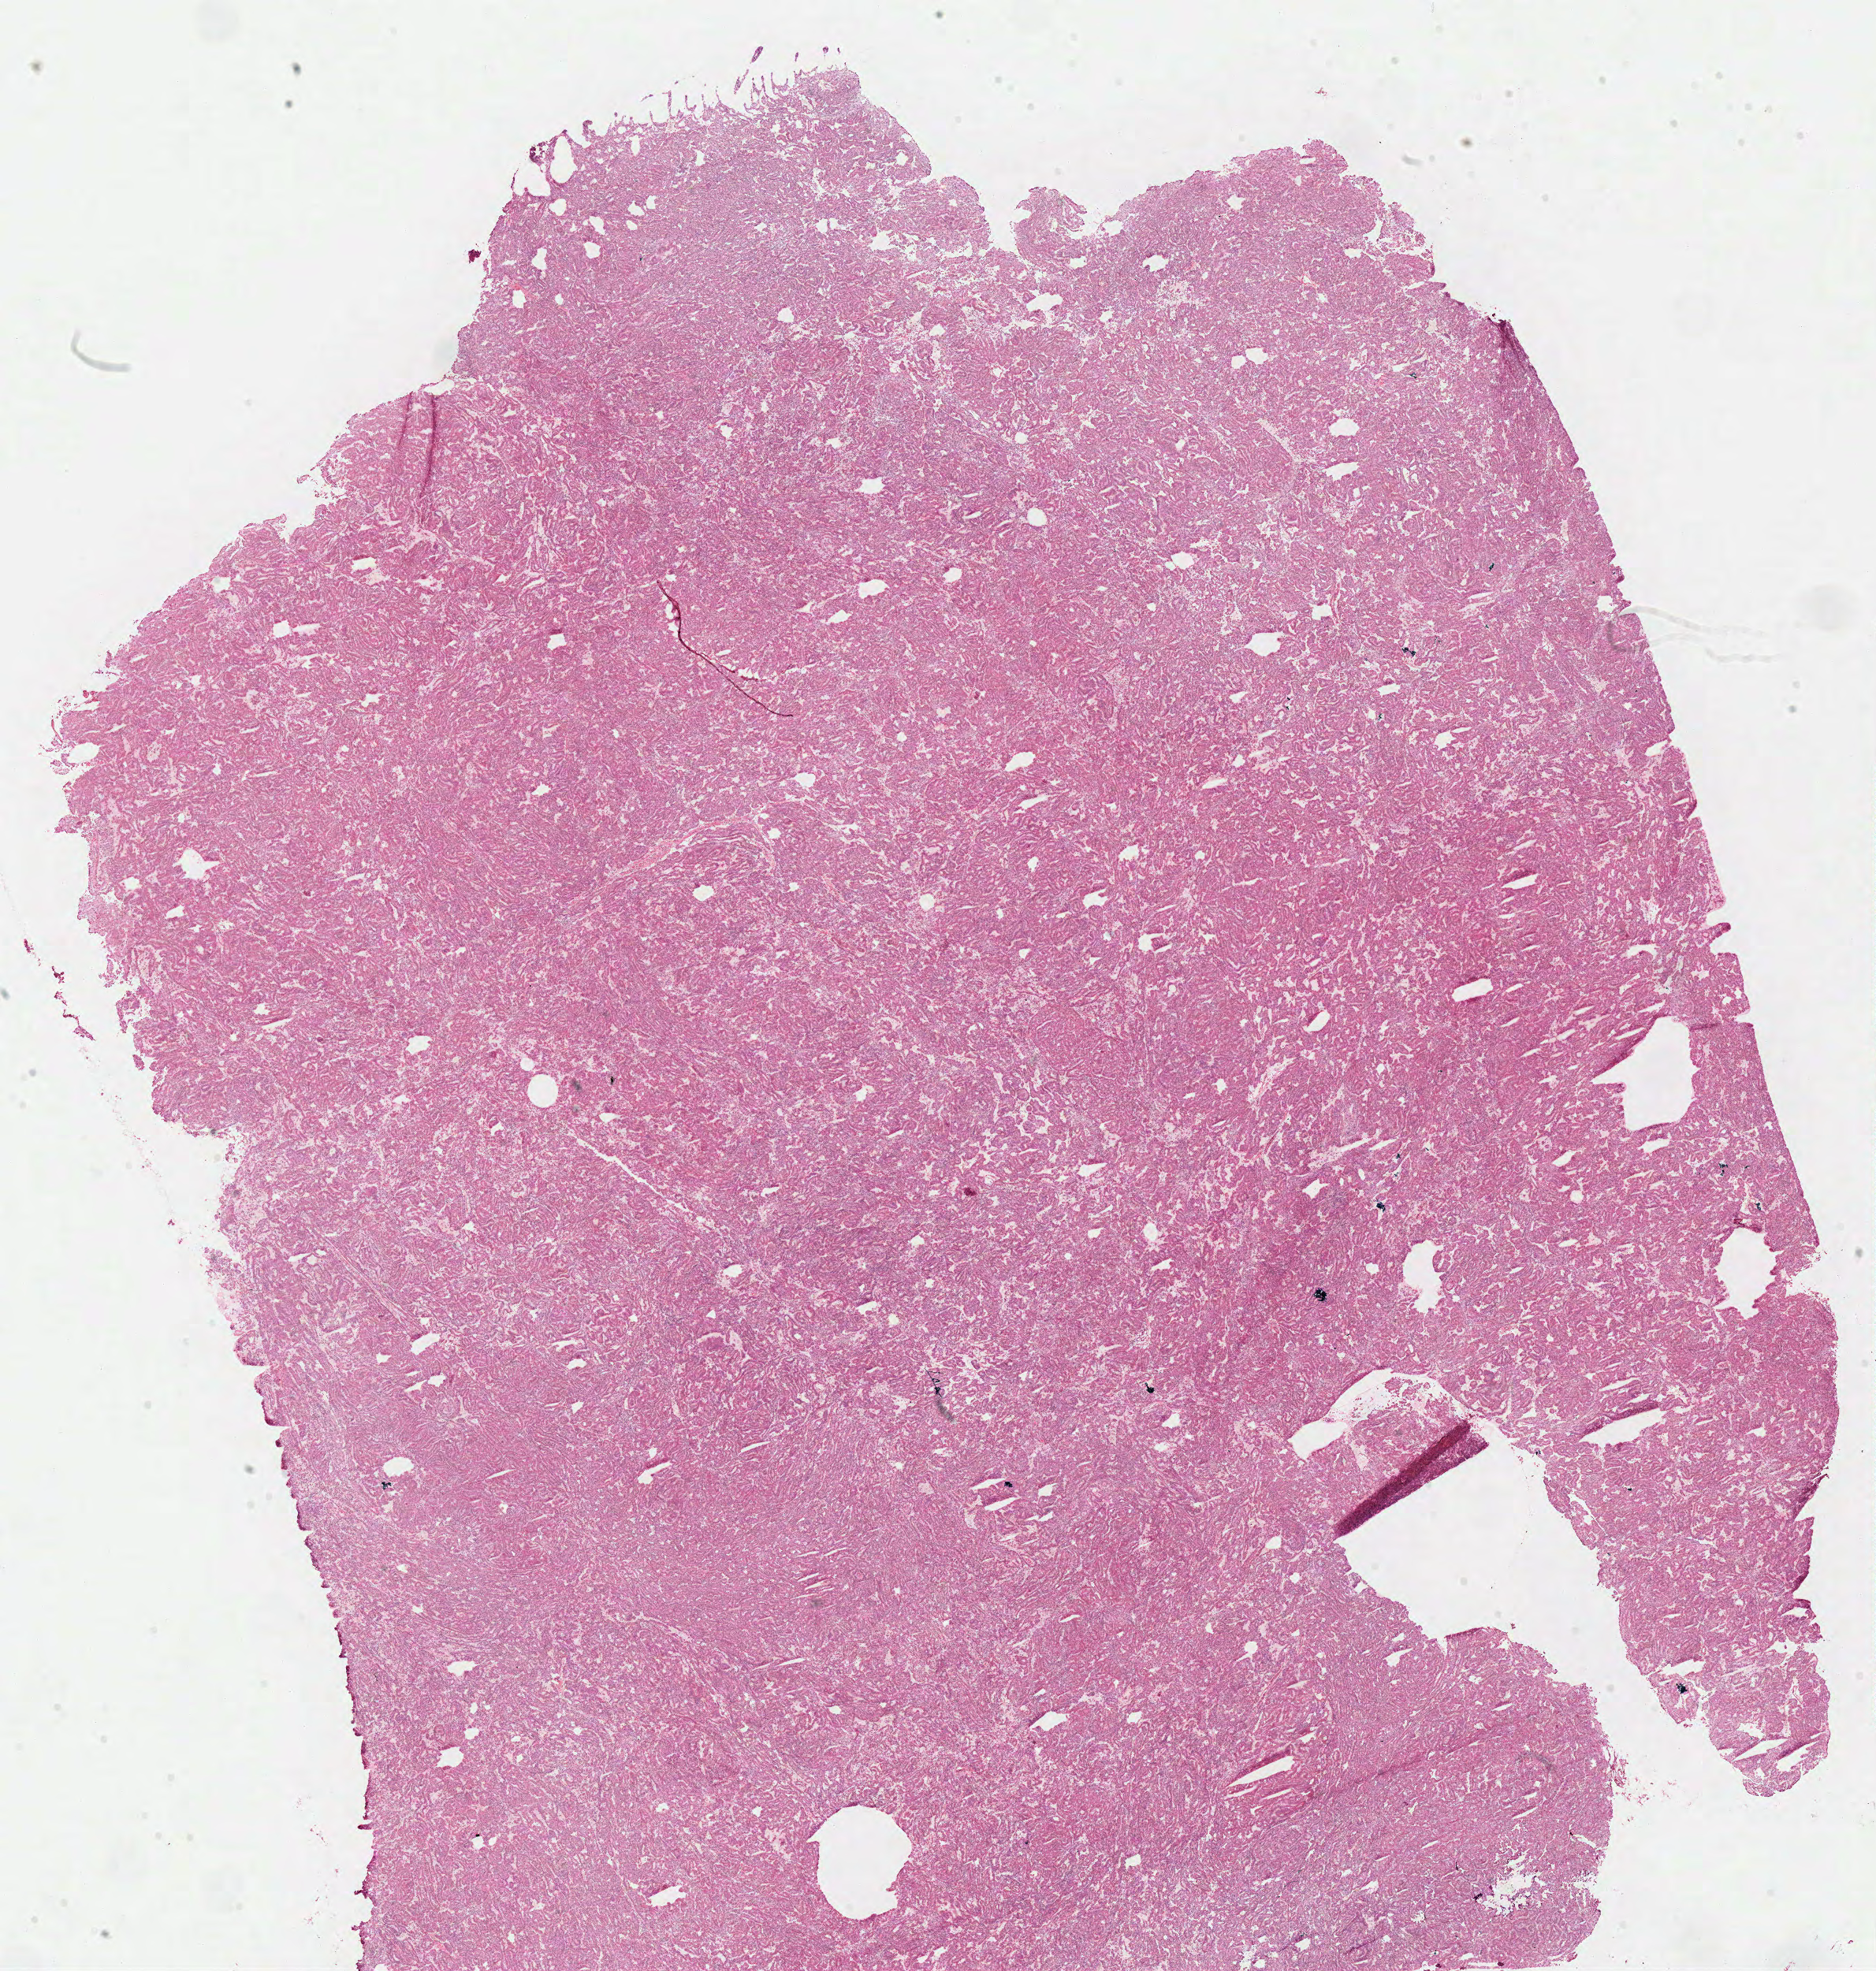
Digitized H&E-stained tissue section (whole slide), shown as a low-resolution overview of the whole scanned area (about 18.8 x 19.7 mm, slide scanned at 40x); frozen section from the top of the tissue portion; sample: primary tumour, kidney. Female patient; age at initial diagnosis 57 years. Pathologist review of this section (percent, as recorded): tumour cells 95%, tumour nuclei 80%, normal cells 0%, stromal cells 5%, necrosis 0%.
* lymph nodes positive (case pathology): 0 of 11 examined
* AJCC pathologic stage: III
* laterality: right
* diagnosis: Papillary adenocarcinoma, NOS